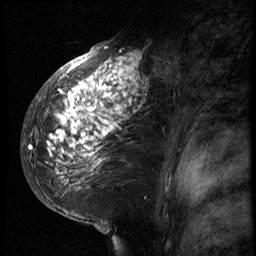
Breast MRI (dynamic contrast-enhanced), one sagittal slice. Slice 42 of 66 in the series (ordered by position). 3 images stored at this slice position (order not interpretable as contrast timing). 1.5 T. TE 4.2 ms, TR 8.9 ms. 2.5 mm slice thickness. 256 × 256 image matrix, field of view 200 × 200 mm. Female patient, age 39 years. From the clinical record (not read from this slice): setting: breast cancer imaged before/during neoadjuvant chemotherapy; receptor status: HER2-positive.
Annotated regions visible in this slice (semi-automatic segmentation, software-assisted and operator-edited):
- analysis volume of interest (the breast-tissue region the enhancement analysis was run in; not a lesion): box from (x=29, y=44) to (x=166, y=196) px
- tumour enhancement mask (voxels above the 140 % enhancement threshold inside the analysis volume of interest): (x=29, y=46)–(x=149, y=181)